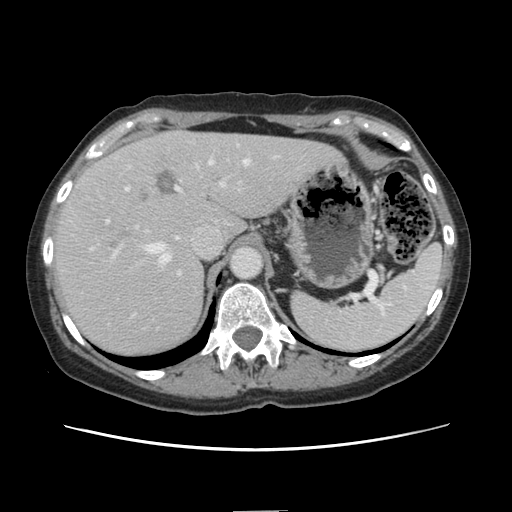
Contrast-enhanced abdominal CT, one axial slice. Position 103 of 141 along the scan axis. Soft-tissue window (W 400 / L 40 HU). 512 × 512 image matrix. Female patient, age 63 years. Case-level facts recorded for this patient, not image findings: diagnosis: colorectal cancer liver metastases, imaged before liver resection; multiple liver metastases: yes; largest metastasis: 3.2 cm; disease in both lobes: yes.
Outlined on this slice (expert manual segmentation):
- hepatic veins: bounding box (x1, y1, x2, y2) in pixels: (144, 159, 249, 263)
- liver: (53, 132, 337, 357)
- planned liver remnant (the part of the liver to remain after resection): (186, 133, 338, 238)
- portal vein (with intrahepatic branches): (125, 182, 226, 274)